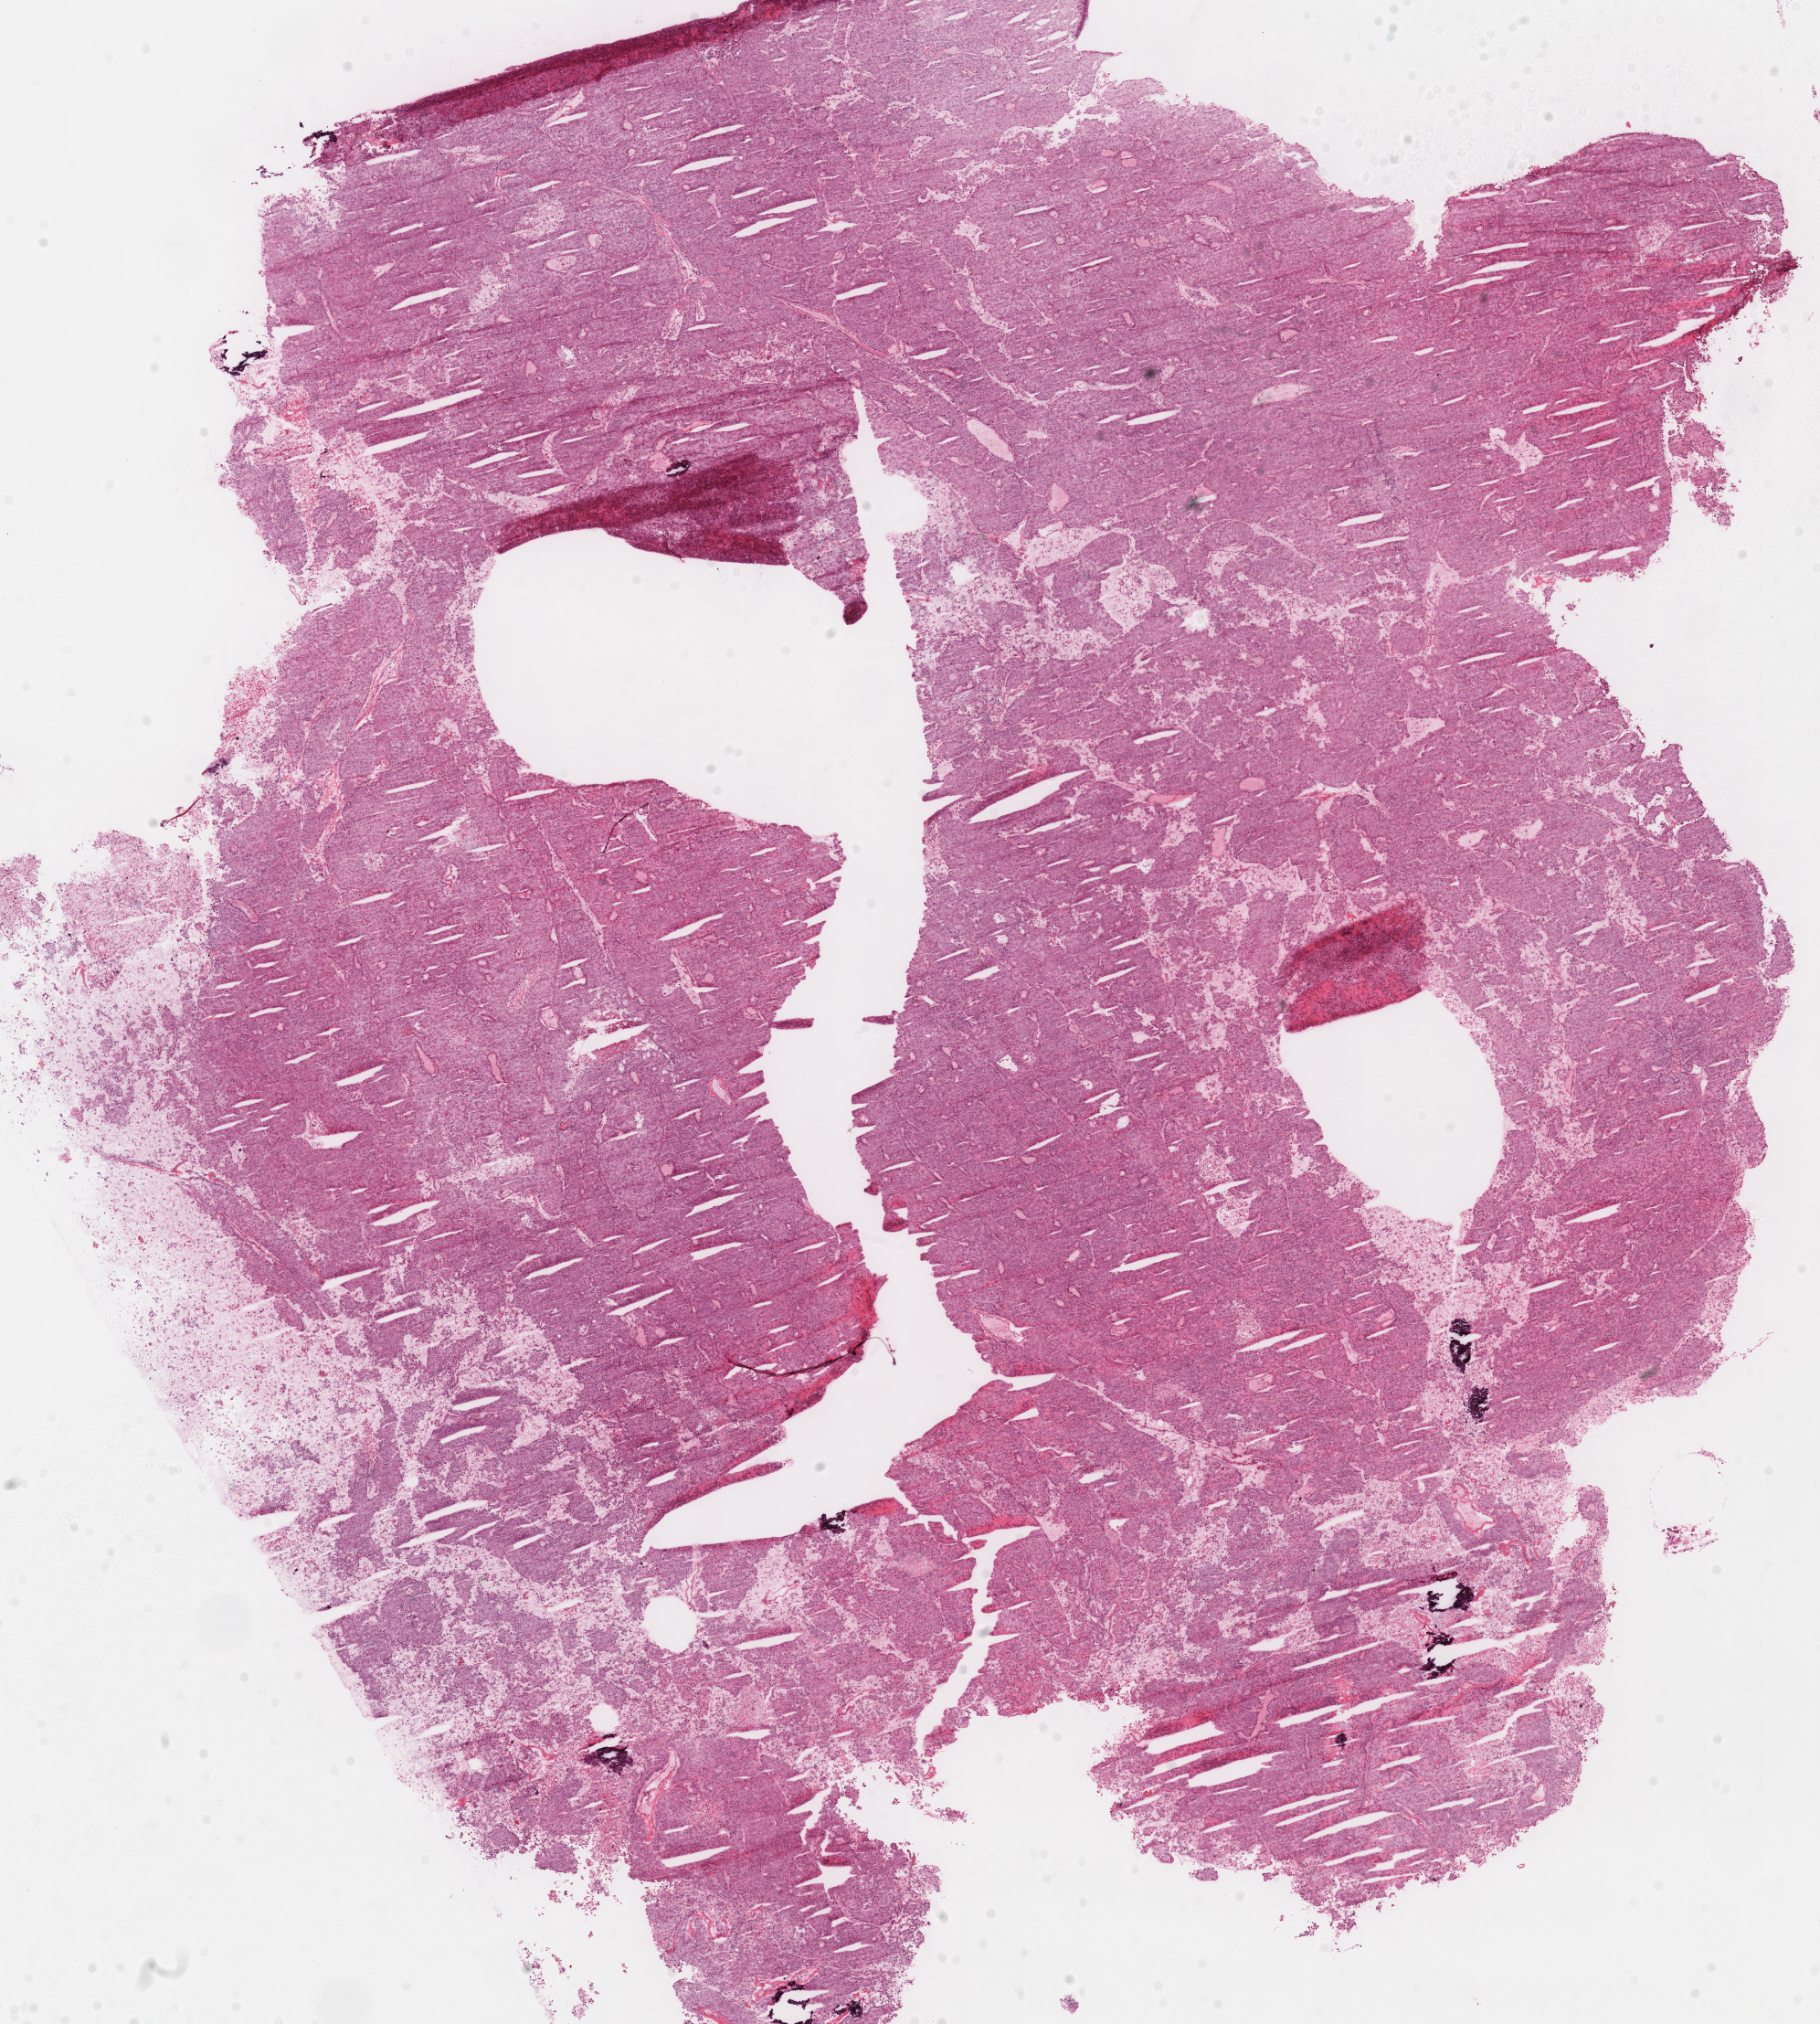
H&E whole-slide image, low-resolution overview of the scanned area, about 15.7 x 17.4 mm, frozen section from the top of the tissue portion, kidney, primary tumour sample. Male, age 41 years at initial diagnosis. Slide review estimates, as recorded: tumour cells 85%, tumour nuclei 95%, normal cells 0%, stromal cells 5%, necrosis 10%.
• laterality: left
• AJCC pathologic stage: IV
• lymph nodes positive (case pathology): 2 of 30 examined
• pathologic diagnosis: Renal cell carcinoma, chromophobe type